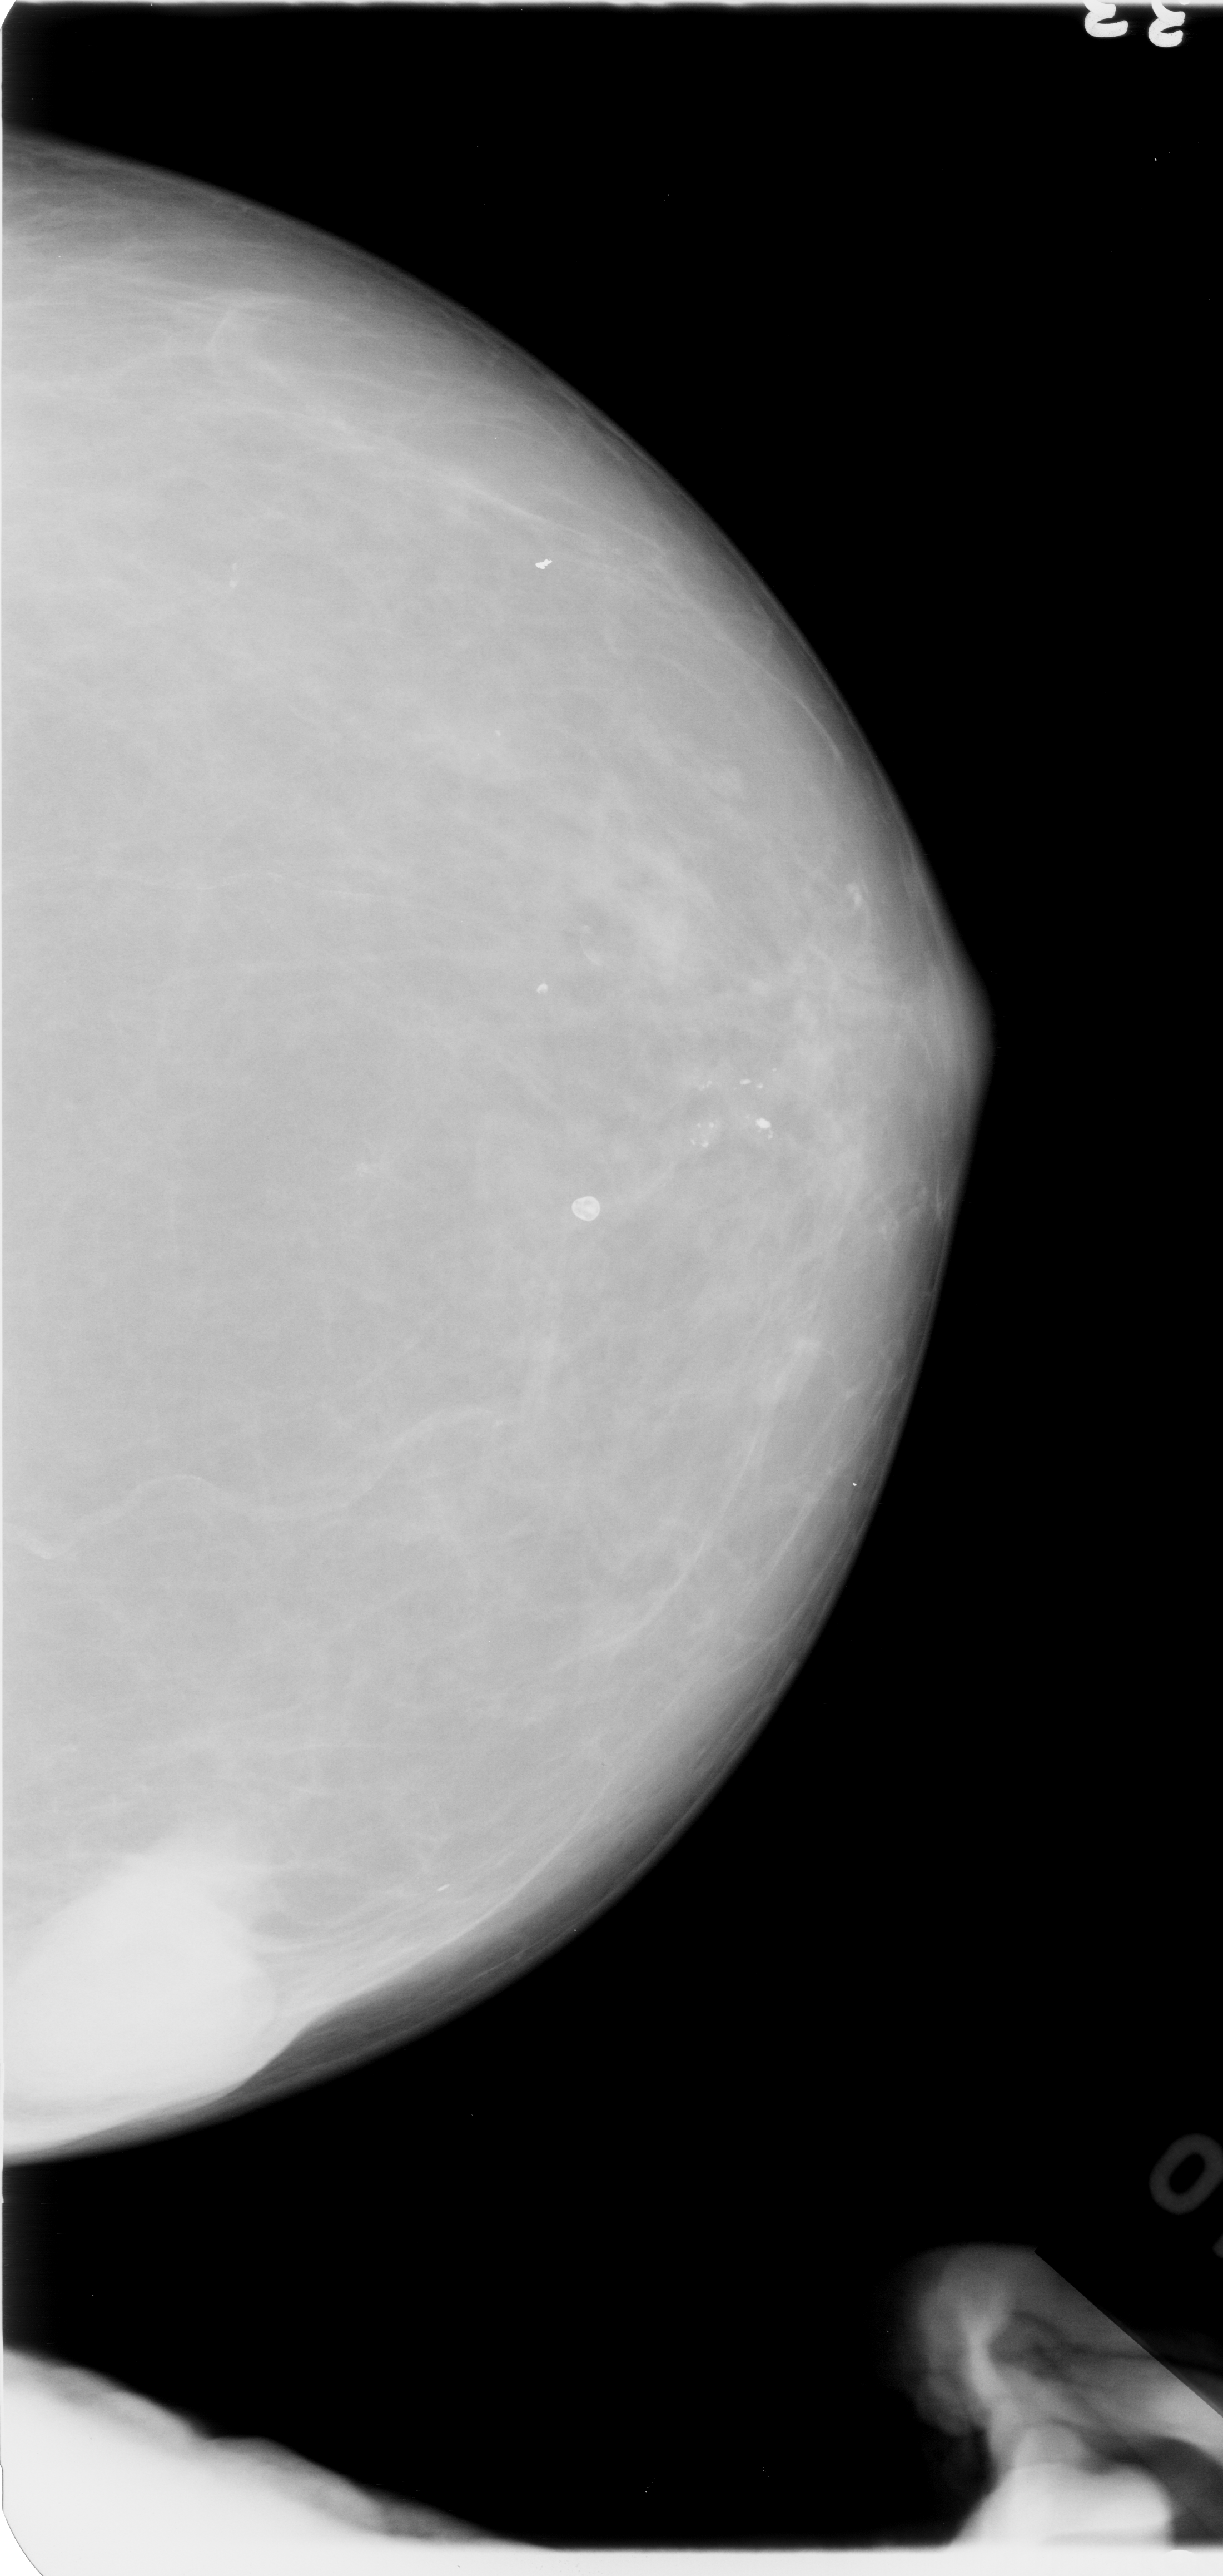
Digitized screen-film mammogram; left breast; craniocaudal (CC) view.
Finding: mass, shape irregular, margins circumscribed / ill defined; BI-RADS assessment category 4; pathology (as recorded): malignant.